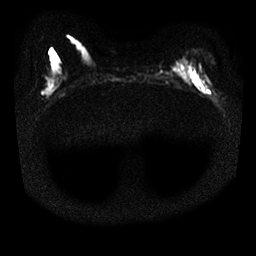
Breast MRI, one axial slice; position 8 of 25 along the scan axis; diffusion-weighted series; image 2 of 4 stored at this slice position (different b-values; order by instance number); 1.5 T; 4 mm slice thickness; 256 × 256 image matrix, field of view 310 × 310 mm. Female patient.
Annotated regions visible in this slice (outlined manually by an expert reader):
- tumour on diffusion-weighted imaging: box from (x=190, y=77) to (x=195, y=80) px